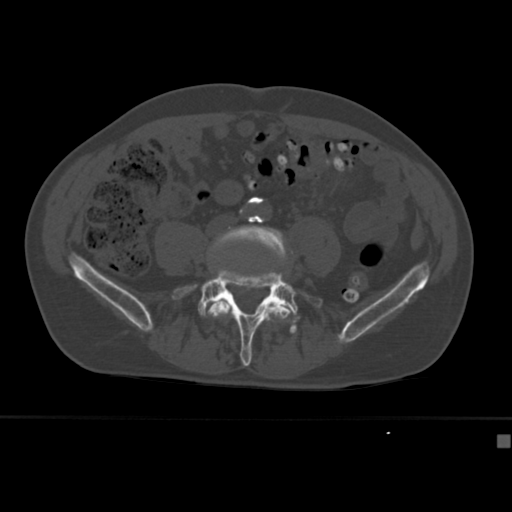
CT including the spine, one axial slice; slice 93 of 430 in the series (ordered by position); bone window (W 1800 / L 400 HU); 1.5 mm slice thickness; 512 × 512 image matrix, field of view 337 × 337 mm. Male patient, age 64 years. Case-level facts recorded for this patient, not image findings: primary cancer: uterus.
Annotated regions visible in this slice (semi-automatically segmented with operator editing):
- L4 vertebra: bounding box <206,225,292,322> (left, top, right, bottom; pixels)
- L5 vertebra: <172,269,323,367>